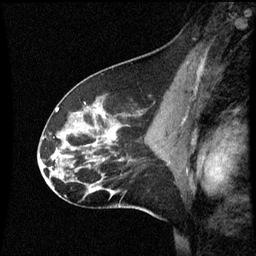
Breast MRI (dynamic contrast-enhanced), one sagittal slice. Position 32 of 60 along the scan axis. Dynamic contrast-enhanced series, image 2 of 3 at this slice position (ordered by acquisition). 1.5 T. TE 4.2 ms, TR 8.9 ms. 2 mm slice thickness. 256 × 256 image matrix, field of view 200 × 200 mm. Female patient, age 45 years. Case-level facts recorded for this patient, not image findings: setting: breast cancer imaged before/during neoadjuvant chemotherapy; receptor status: HR-positive, HER2-negative.
Outlined on this slice (semi-automatic segmentation, software-assisted and operator-edited):
- analysis volume of interest (the breast-tissue region the enhancement analysis was run in; not a lesion): bounding box <46,94,171,205> (left, top, right, bottom; pixels)
- tumour enhancement mask (voxels above the 70 % enhancement threshold inside the analysis volume of interest): <56,108,117,139>